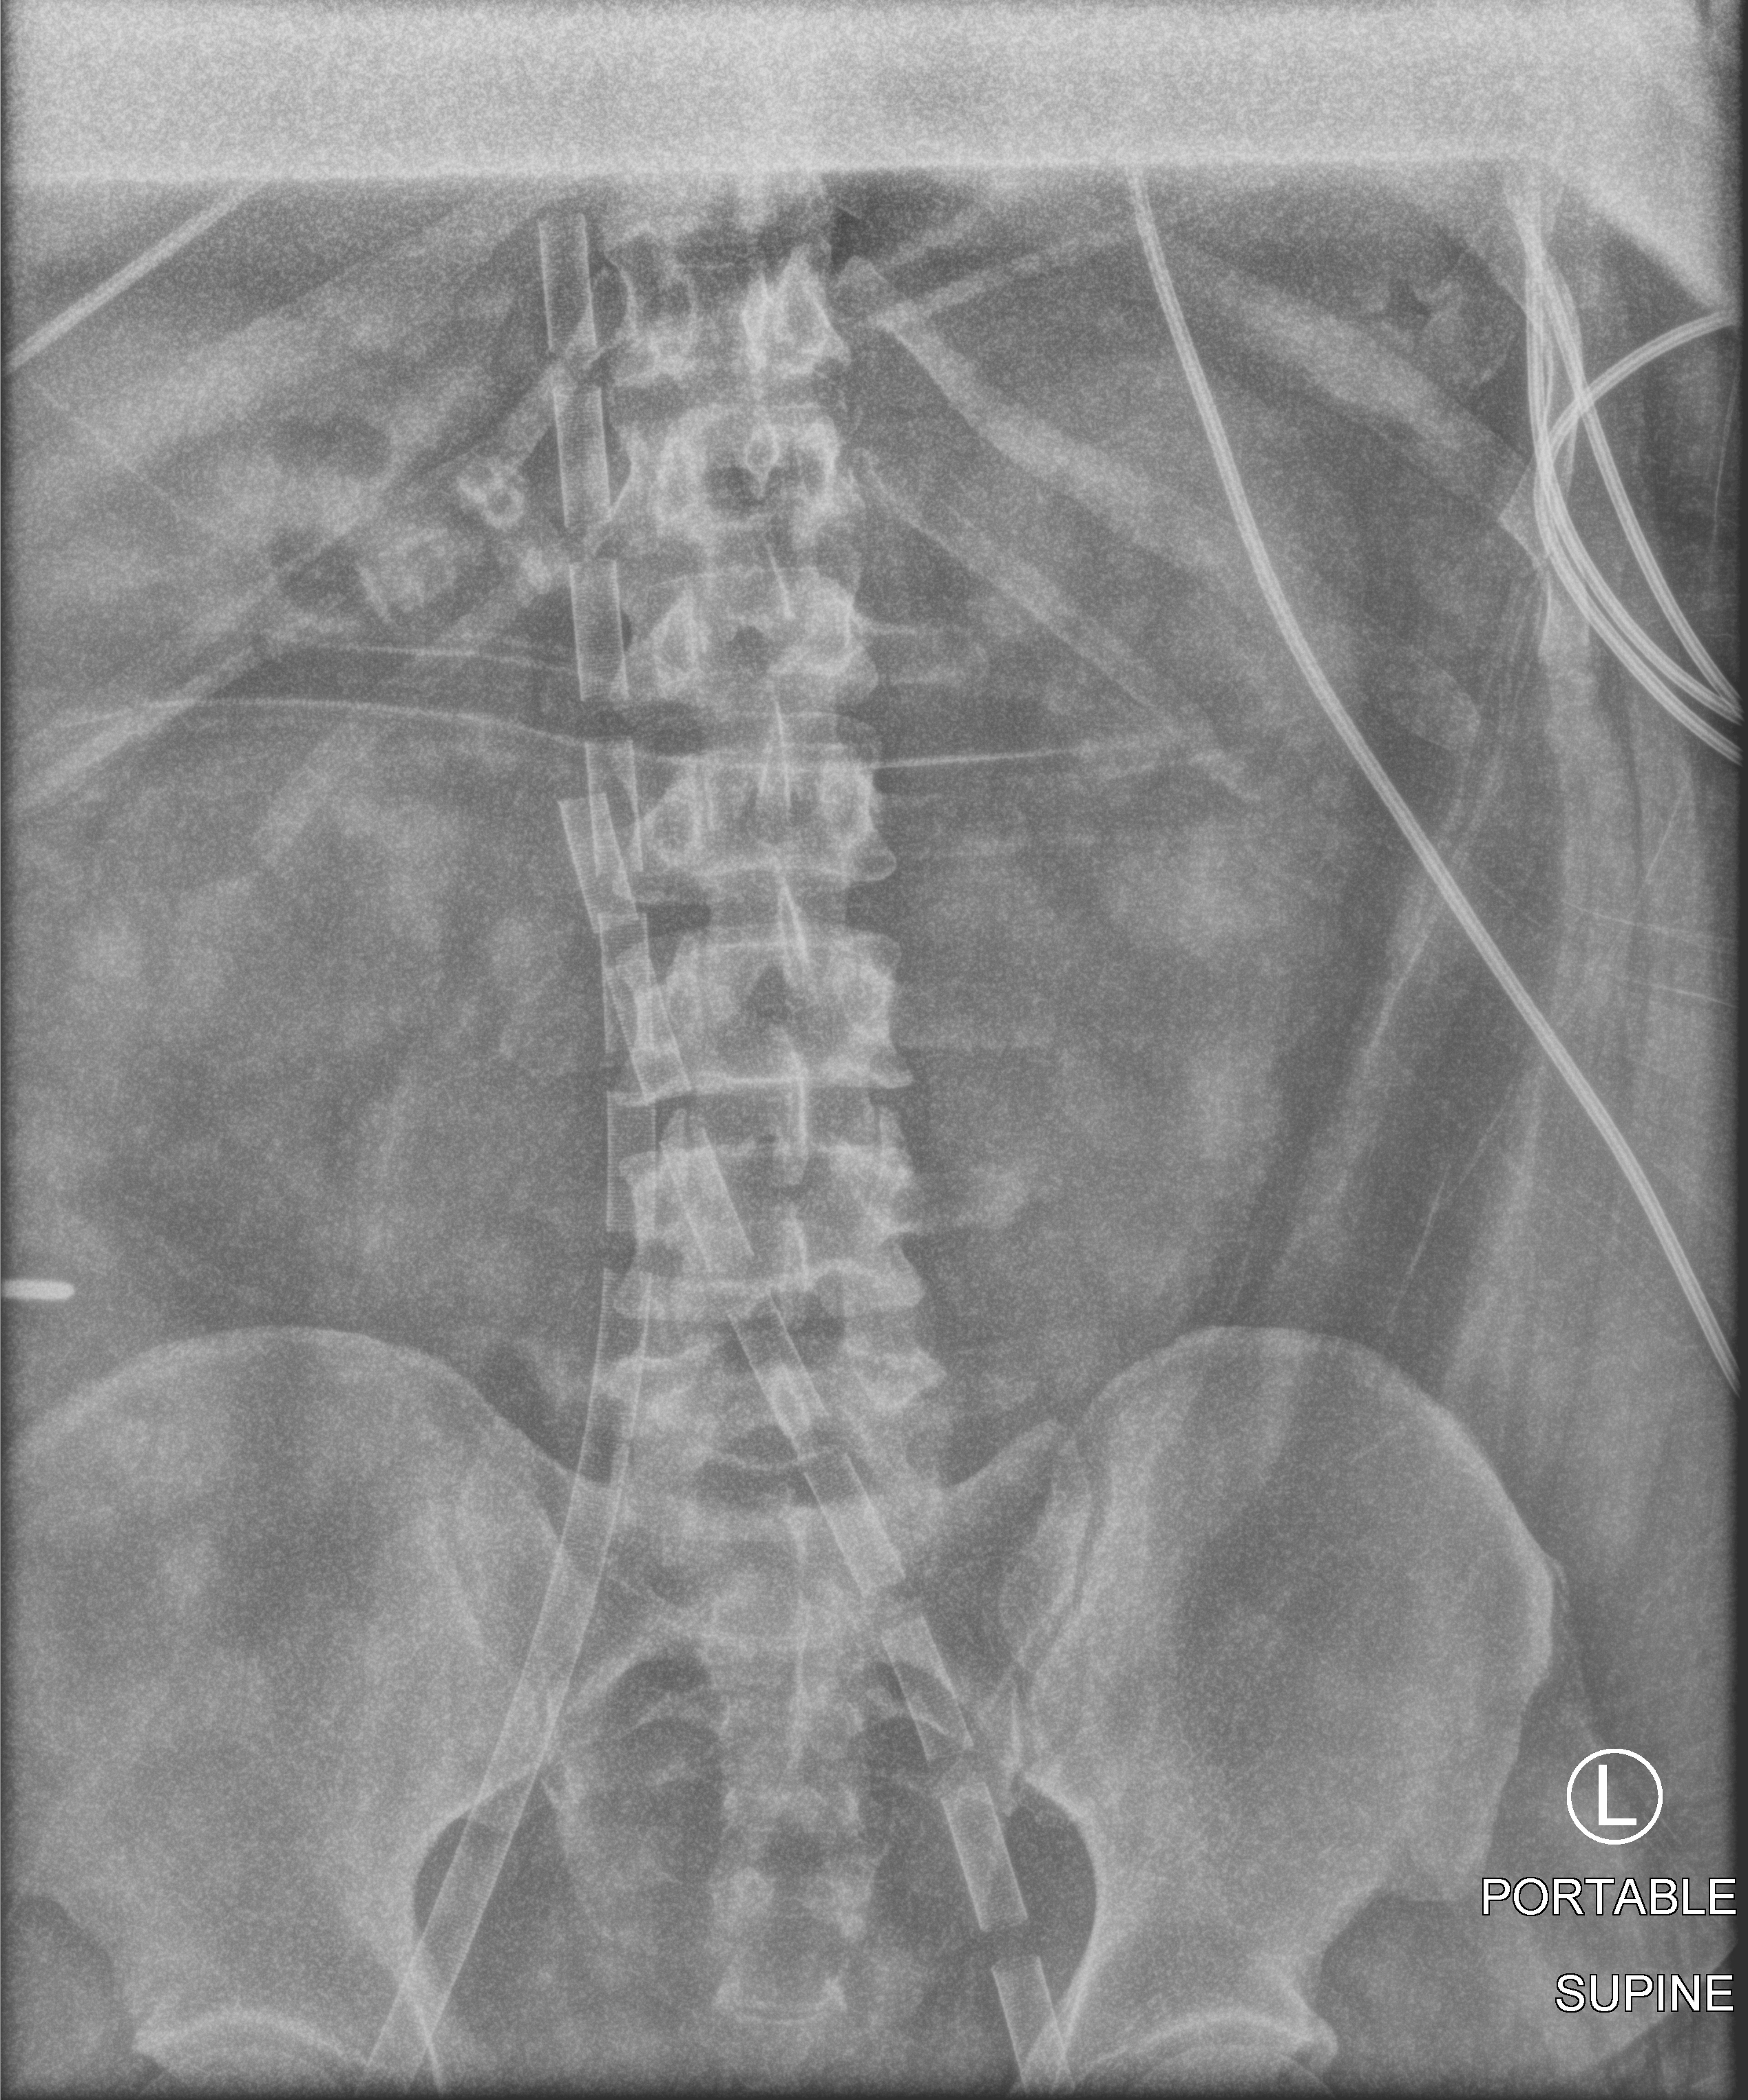
Bedside abdomen radiograph (computed radiography), anteroposterior (AP) projection. Patient hospitalised with COVID-19, aged 18–59 years.
From the hospital-stay record, not from the radiograph (when in the stay this image was taken is not recorded): other chronic lung disease (admission record): no; mechanically ventilated during this hospital stay: yes; admitted to intensive care during this hospital stay: yes.